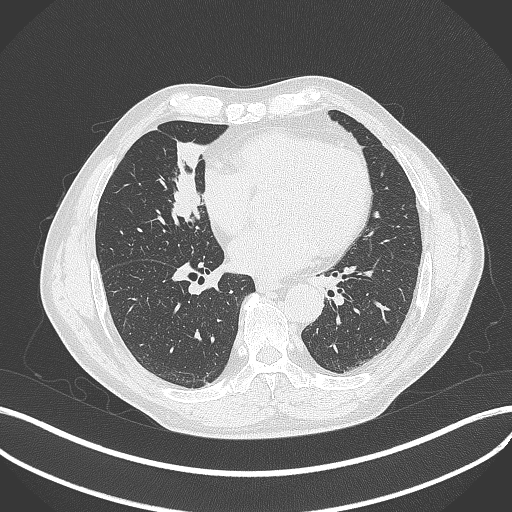
Chest CT, one axial slice; slice 166 of 429 in the series (ordered by position); reconstruction kernel B70f; 120 kVp; lung window (W 1500 / L -600 HU); 1 mm slice thickness; 512 × 512 image matrix, field of view 400 × 400 mm. Male patient, age 61 years. Case-level facts recorded for this patient, not image findings: clinical TNM (as recorded): T2b N1 M0.
Structures marked on this image (bounding box drawn by a radiologist):
- lung tumour (recorded histology: squamous cell carcinoma): bounding box [x1, y1, x2, y2] px = [169, 165, 208, 225]